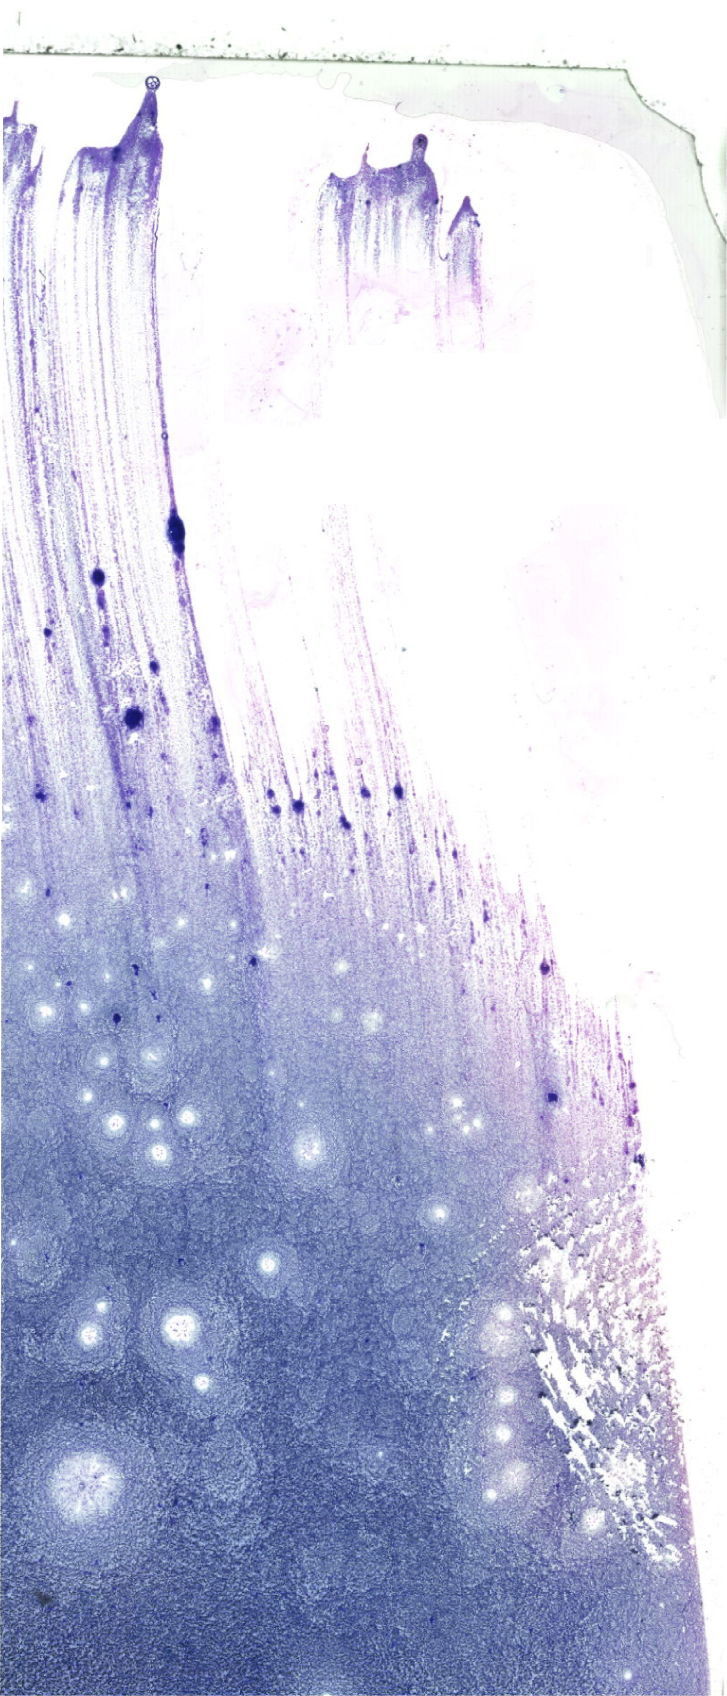
May-Grünwald-Giemsa (MGG)-stained marrow aspirate smear (whole slide), whole scanned area (about 20.6 x 48.1 mm) shown as a low-resolution overview. Male patient.
* diagnosis: Acute Myeloid Leukemia without Maturation